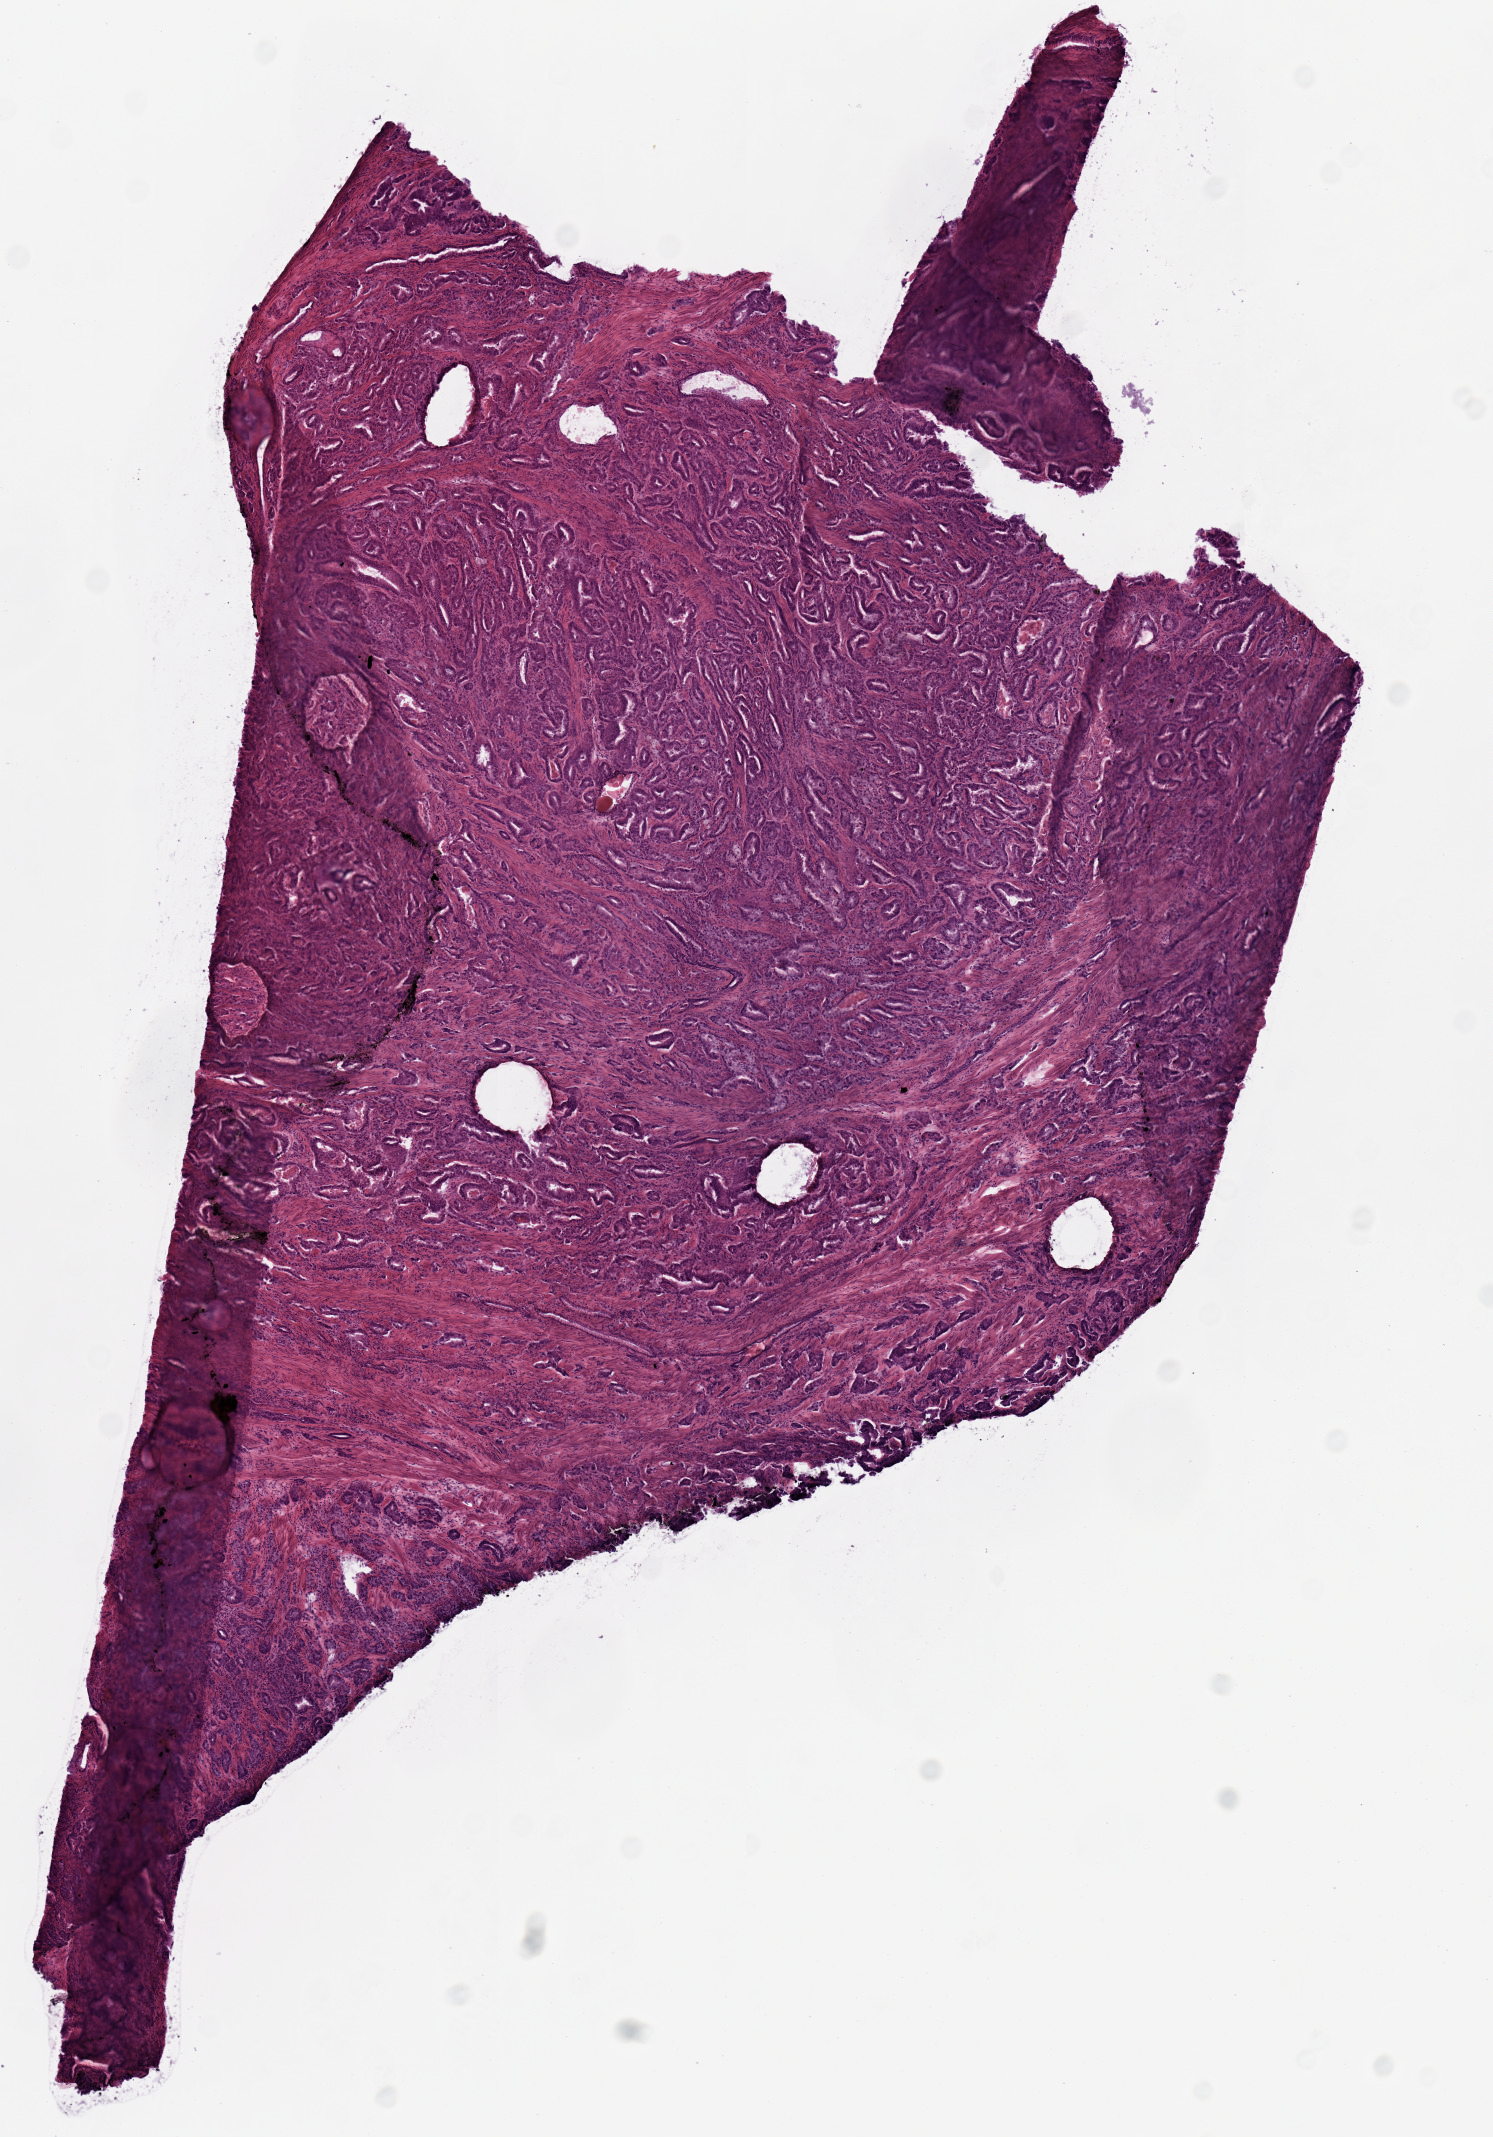
Hematoxylin and eosin (H&E) stained whole-slide image — shown as a low-resolution overview of the whole scanned area (about 5.9 x 8.4 mm, slide scanned at 20x), frozen section from the top of the tissue portion, prostate, primary tumour sample. Male patient; age at initial diagnosis 70 years. Gleason score: 7 (4+3). Pathologist review of this section (percent, as recorded): tumour nuclei 70%, necrosis 0%.
* histologic diagnosis: Acinar cell carcinoma (prostate gland)
* lymph nodes positive (case pathology): 0 of 10 examined
* laterality: right